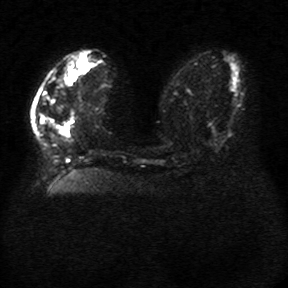
Breast MRI, one axial slice; slice 12 of 34 in the series (ordered by position); diffusion-weighted series; image 2 of 4 stored at this slice position (different b-values; order by instance number); 1.5 T; 5 mm slice thickness; 288 × 288 image matrix, field of view 340 × 340 mm. Female patient.
Structures marked on this image (outlined manually by an expert reader):
- tumour on diffusion-weighted imaging: box from (x=40, y=95) to (x=58, y=141) px